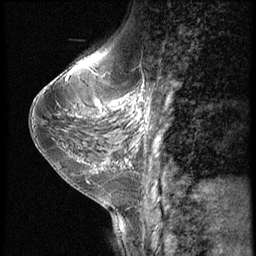
Breast MRI (dynamic contrast-enhanced), one sagittal slice; slice 24 of 56 in the series (ordered by position); dynamic contrast-enhanced series, image 2 of 3 at this slice position (ordered by acquisition); 1.5 T; TE 4.2 ms, TR 9 ms; 2.5 mm slice thickness; 256 × 256 image matrix, field of view 180 × 180 mm. Female patient, age 38 years. Case-level facts recorded for this patient, not image findings: setting: breast cancer imaged before/during neoadjuvant chemotherapy; receptor status: triple-negative.
Annotated regions visible in this slice (semi-automatic segmentation, software-assisted and operator-edited):
- analysis volume of interest (the breast-tissue region the enhancement analysis was run in; not a lesion): bounding box (x1, y1, x2, y2) in pixels: (107, 95, 155, 149)
- tumour enhancement mask (voxels above the 140 % enhancement threshold inside the analysis volume of interest): (110, 95, 148, 129)